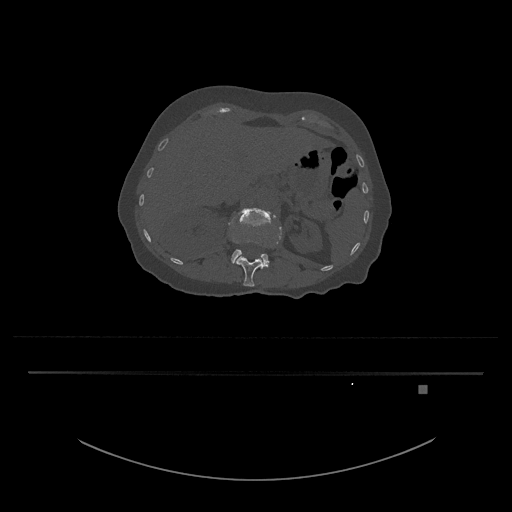
CT including the spine, one axial slice. Position 530 of 797 along the scan axis. Reconstruction kernel Br40s/3. 120 kVp. Bone window (W 1800 / L 400 HU). 0.5 mm slice thickness. 512 × 512 image matrix. Female patient, age 57 years. Case-level facts recorded for this patient, not image findings: primary cancer: cervical.
Structures marked on this image (semi-automatic segmentation, software-assisted and operator-edited):
- L1 vertebra: box from (x=233, y=226) to (x=282, y=287) px